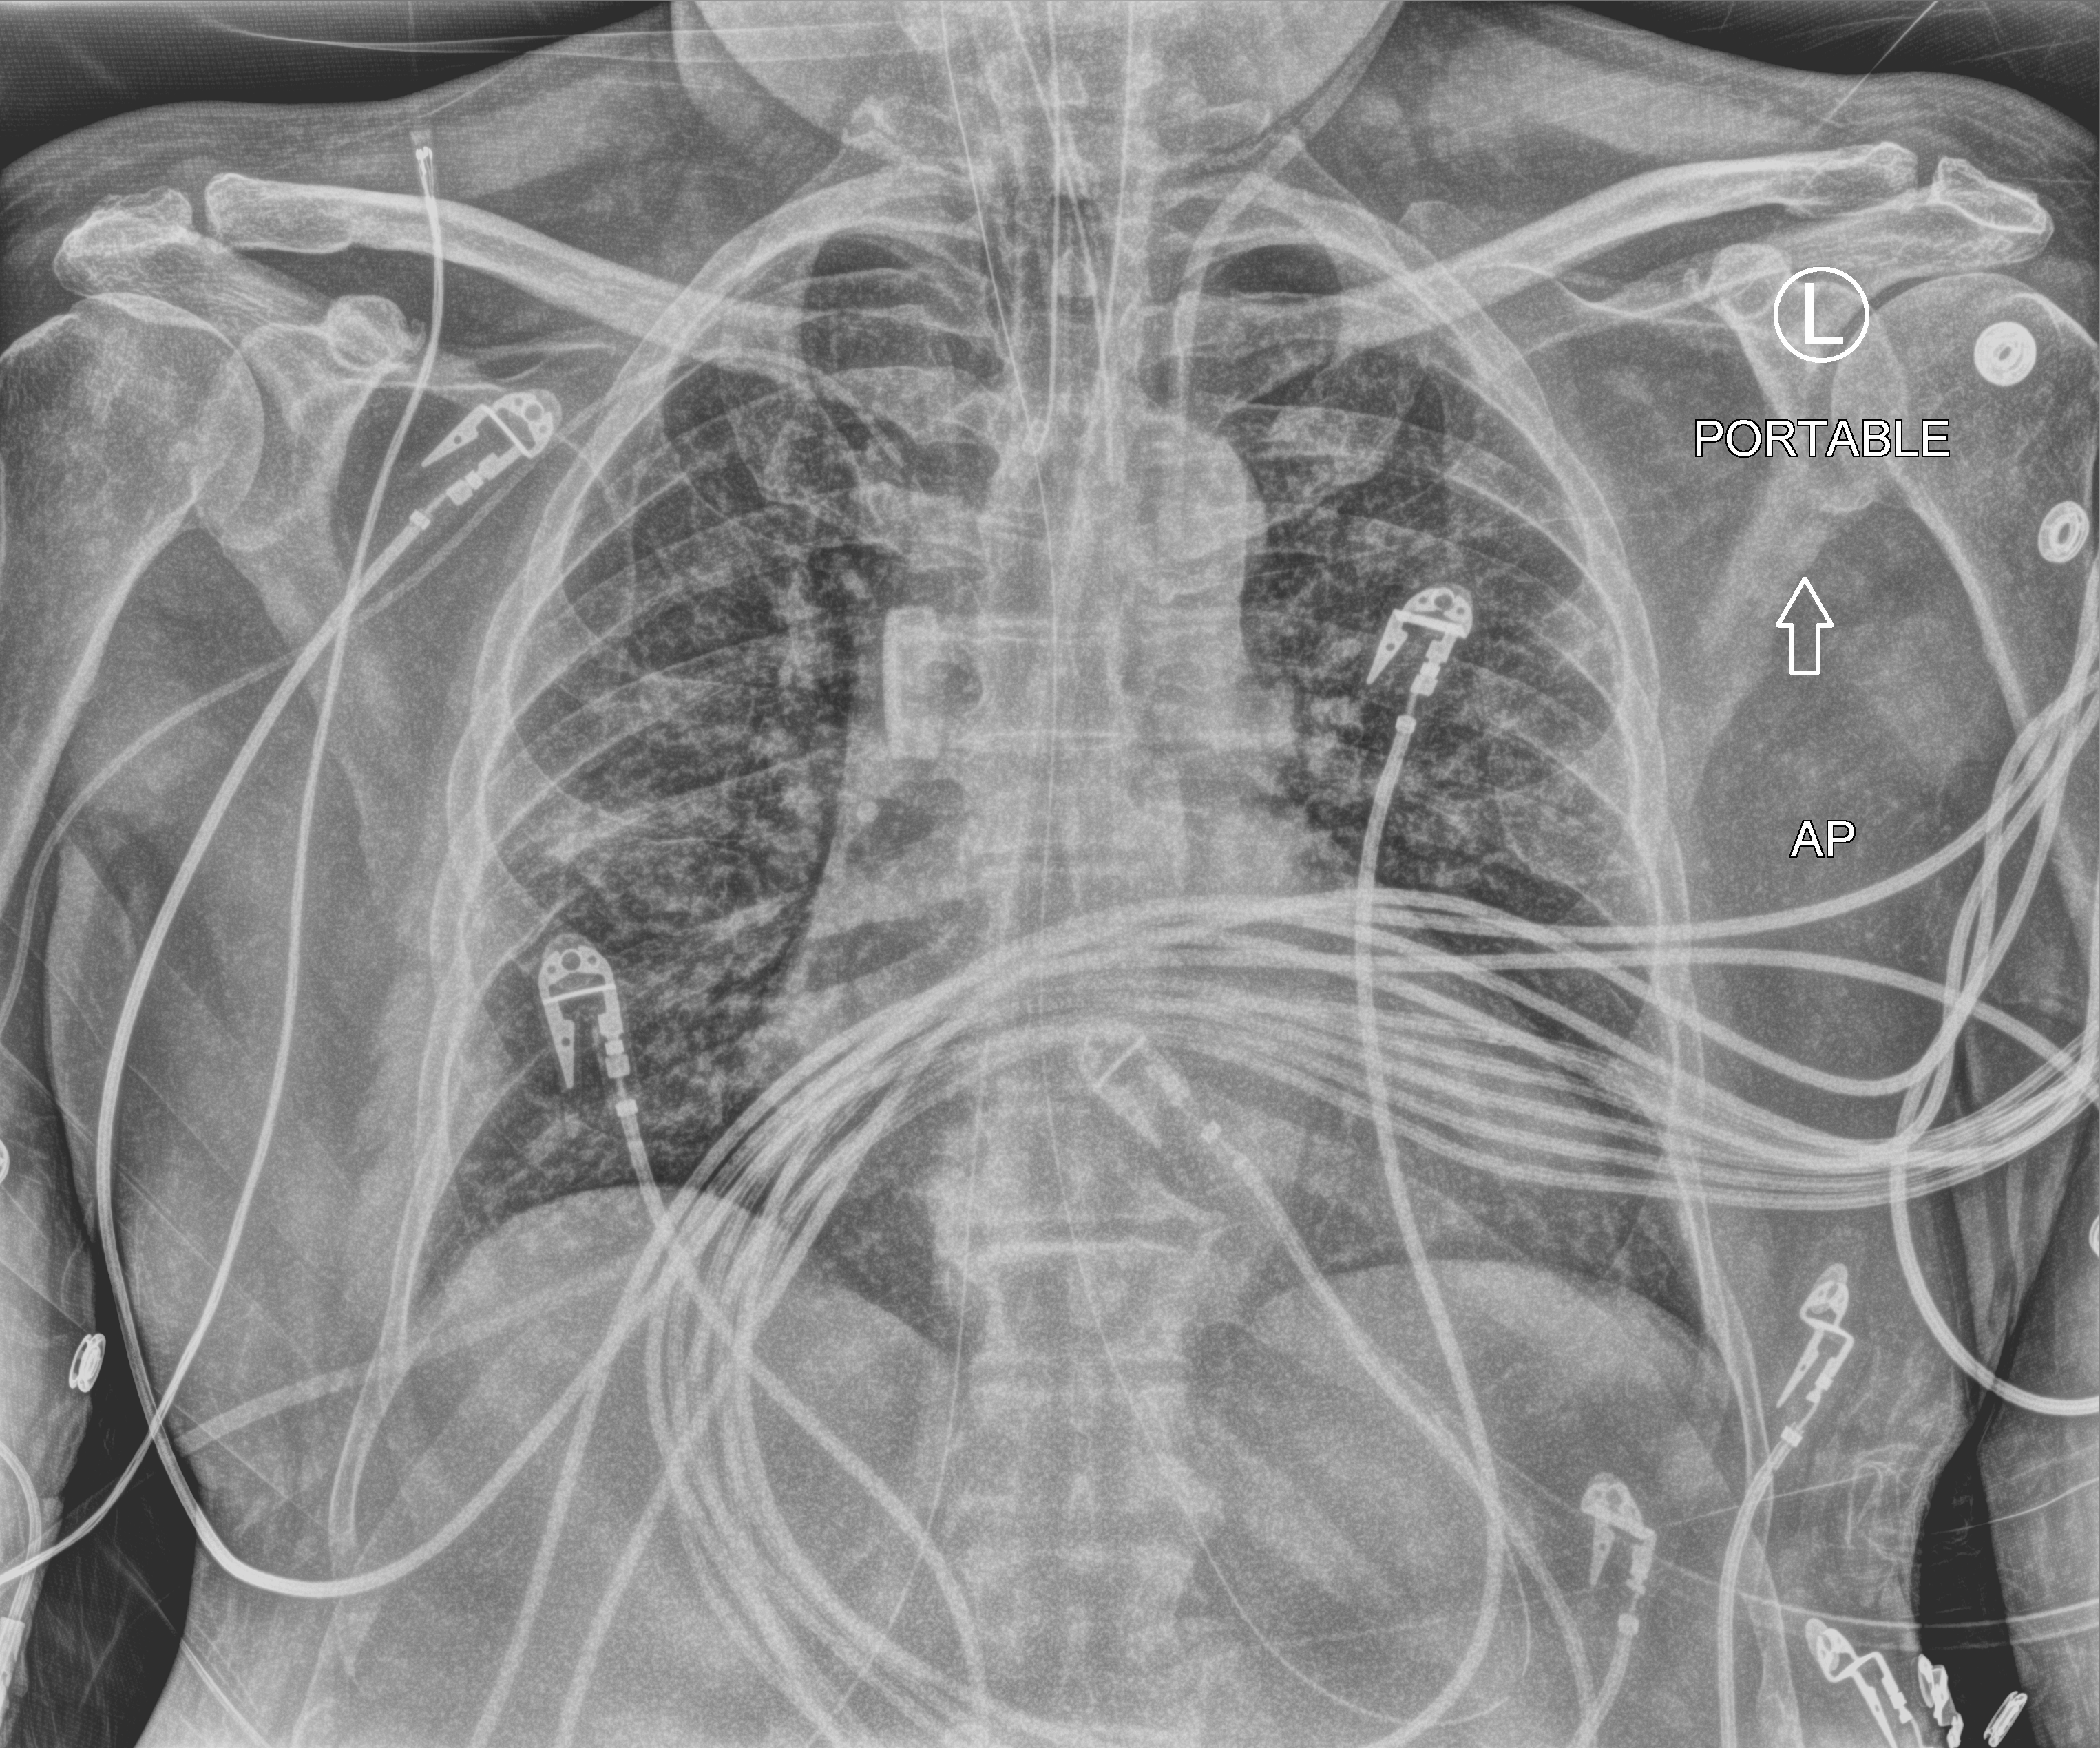
Chest X-ray (portable), anteroposterior (AP) projection. Male patient hospitalised with COVID-19, age 60–74 years.
Admission-level facts for this patient (not findings on this image; timing relative to this image not recorded):
- length of hospital stay: 31 days
- mechanically ventilated during this hospital stay: yes